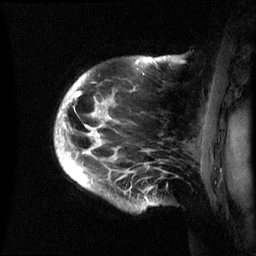
Breast MRI (dynamic contrast-enhanced), one sagittal slice; slice 50 of 60 in the series (ordered by position); dynamic contrast-enhanced series, image 2 of 3 at this slice position (ordered by acquisition); 1.5 T; TE 4.2 ms, TR 8.4 ms; 256 × 256 image matrix, field of view 230 × 230 mm. Female patient, age 48 years.
Structures marked on this image (semi-automatically segmented with operator editing):
- analysis volume of interest (the breast-tissue region the enhancement analysis was run in; not a lesion): bounding box <55,56,179,212> (left, top, right, bottom; pixels)
- tumour enhancement mask (voxels above the 70 % enhancement threshold inside the analysis volume of interest): <59,57,152,202>